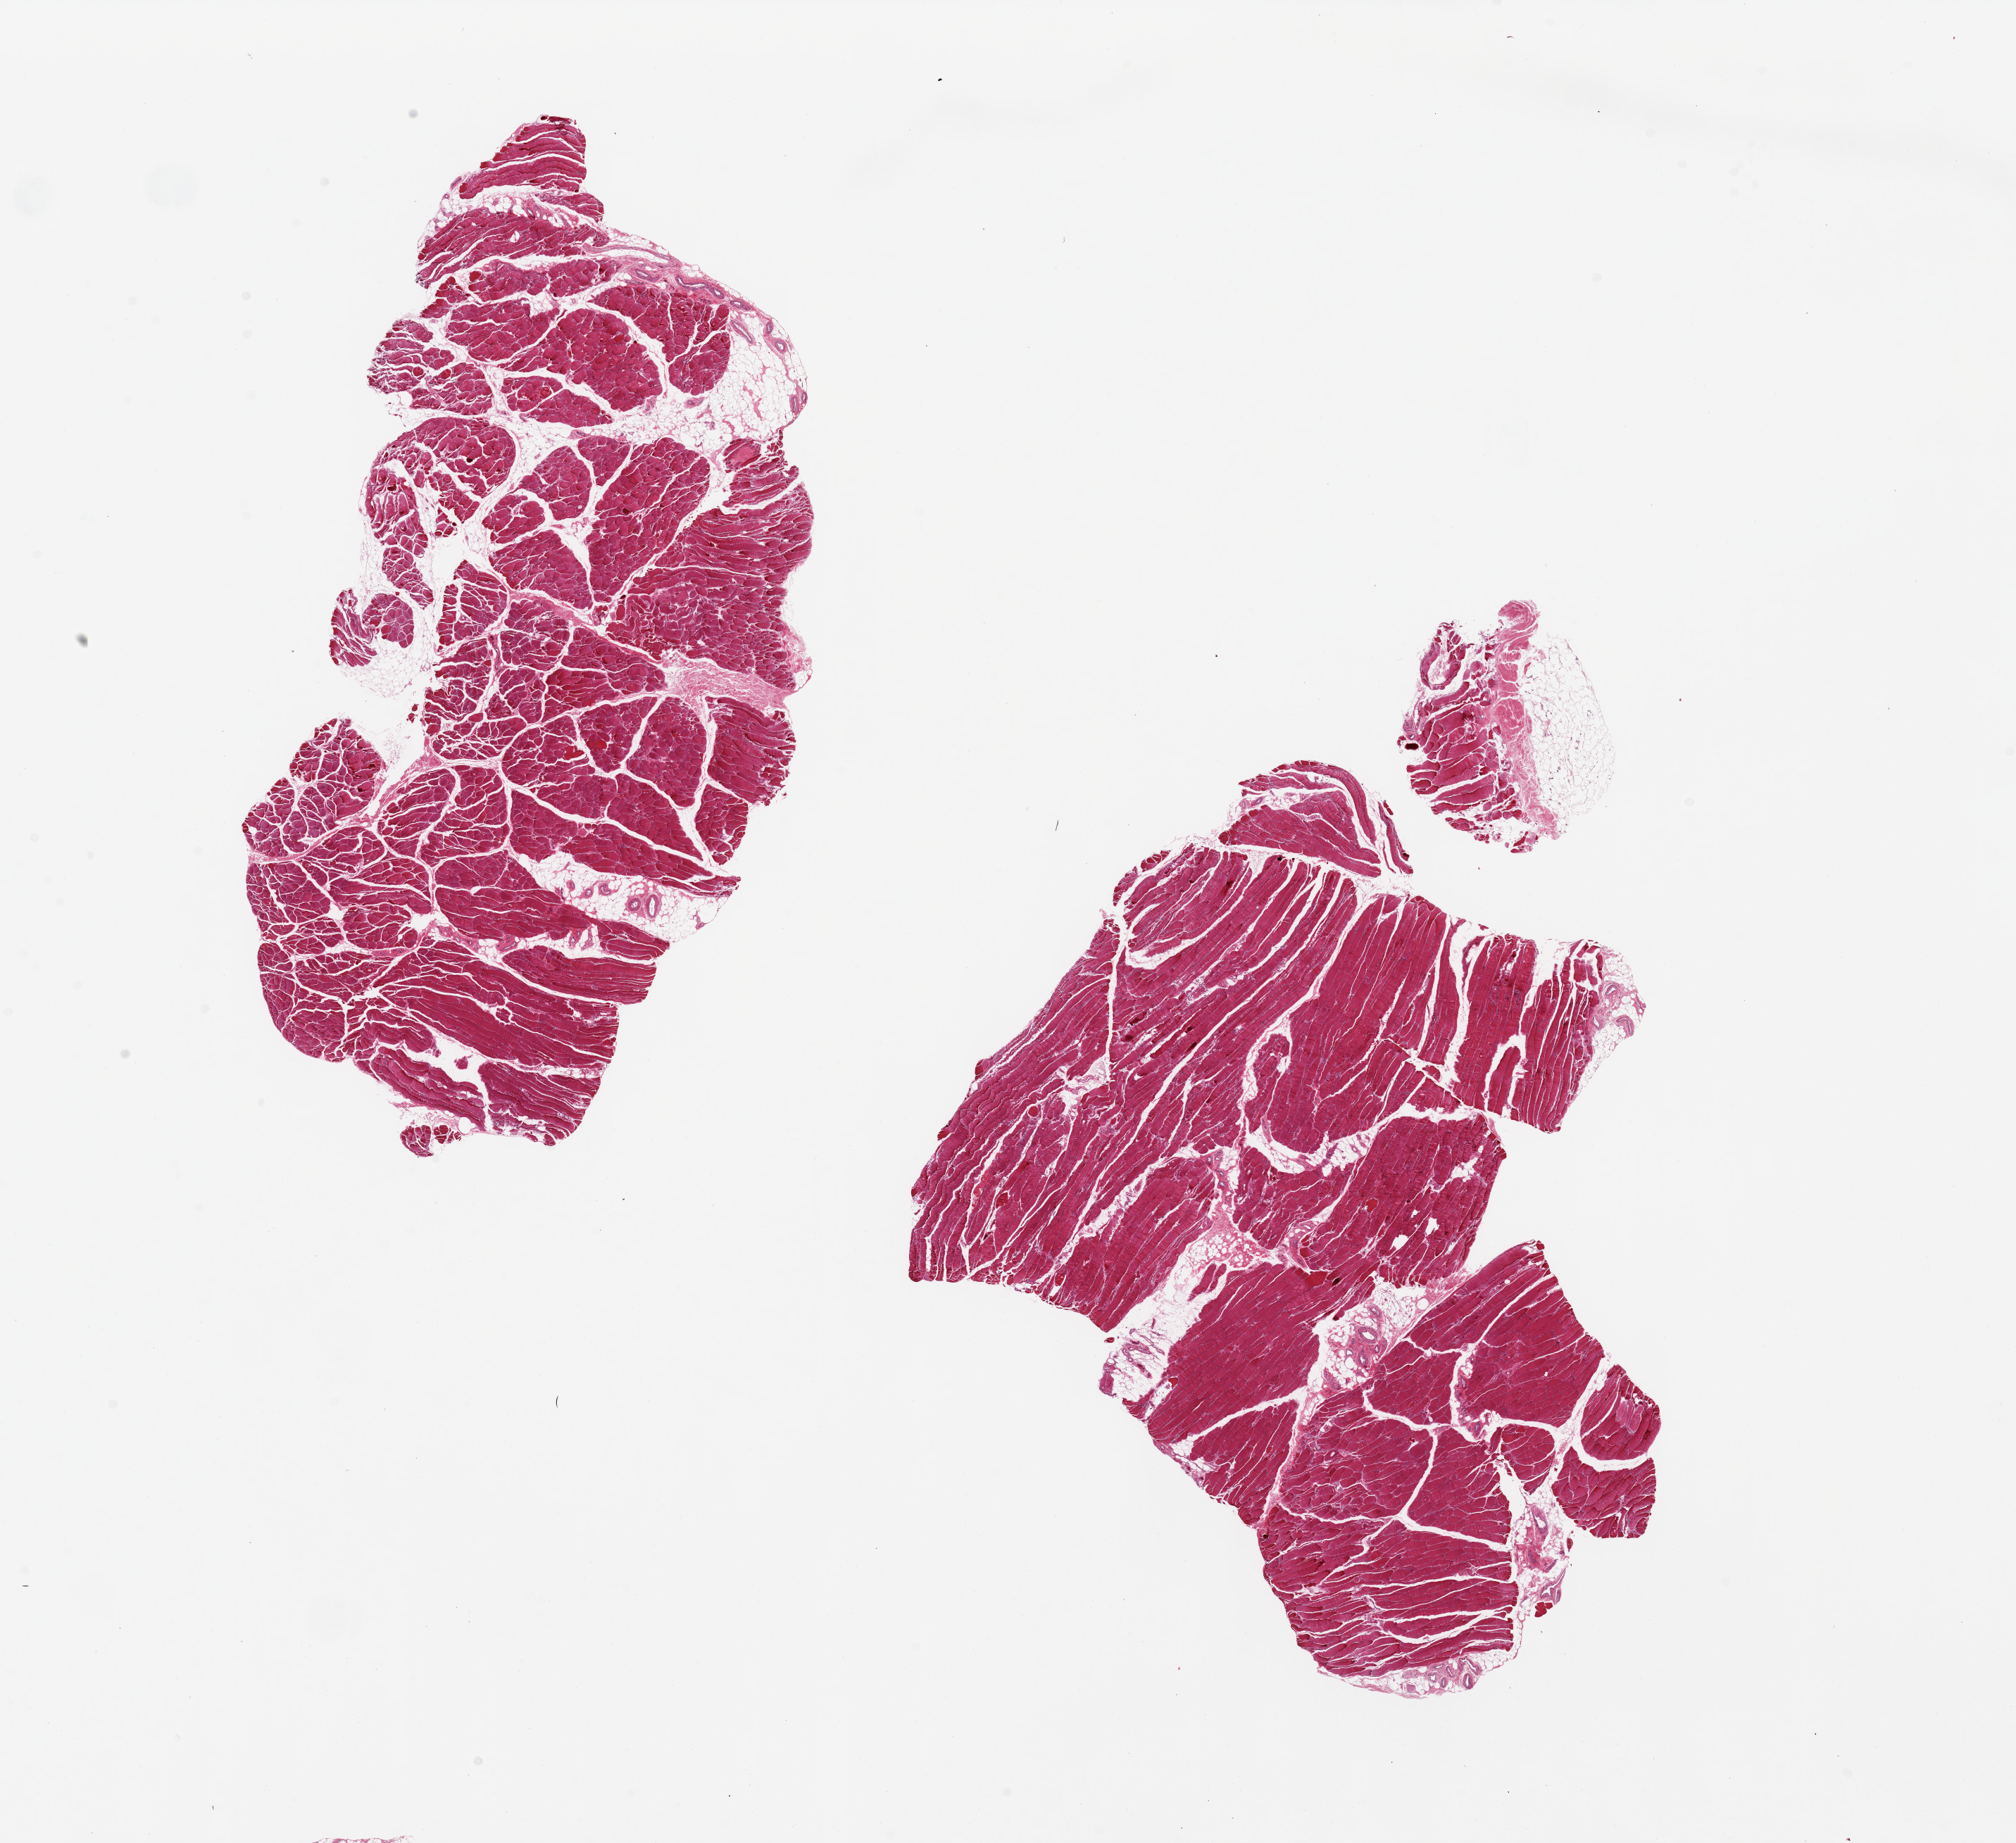
Haematoxylin and eosin whole-slide image — low-resolution overview of the scanned area, about 22.6 x 20.7 mm; PAXgene-fixed, paraffin-embedded tissue; target tissue: skeletal muscle; tissue donor sample. Female donor.
Pathologist's review note for this sample: 2 pieces, 12x6 & 10x9mm; 5% internal adipose.